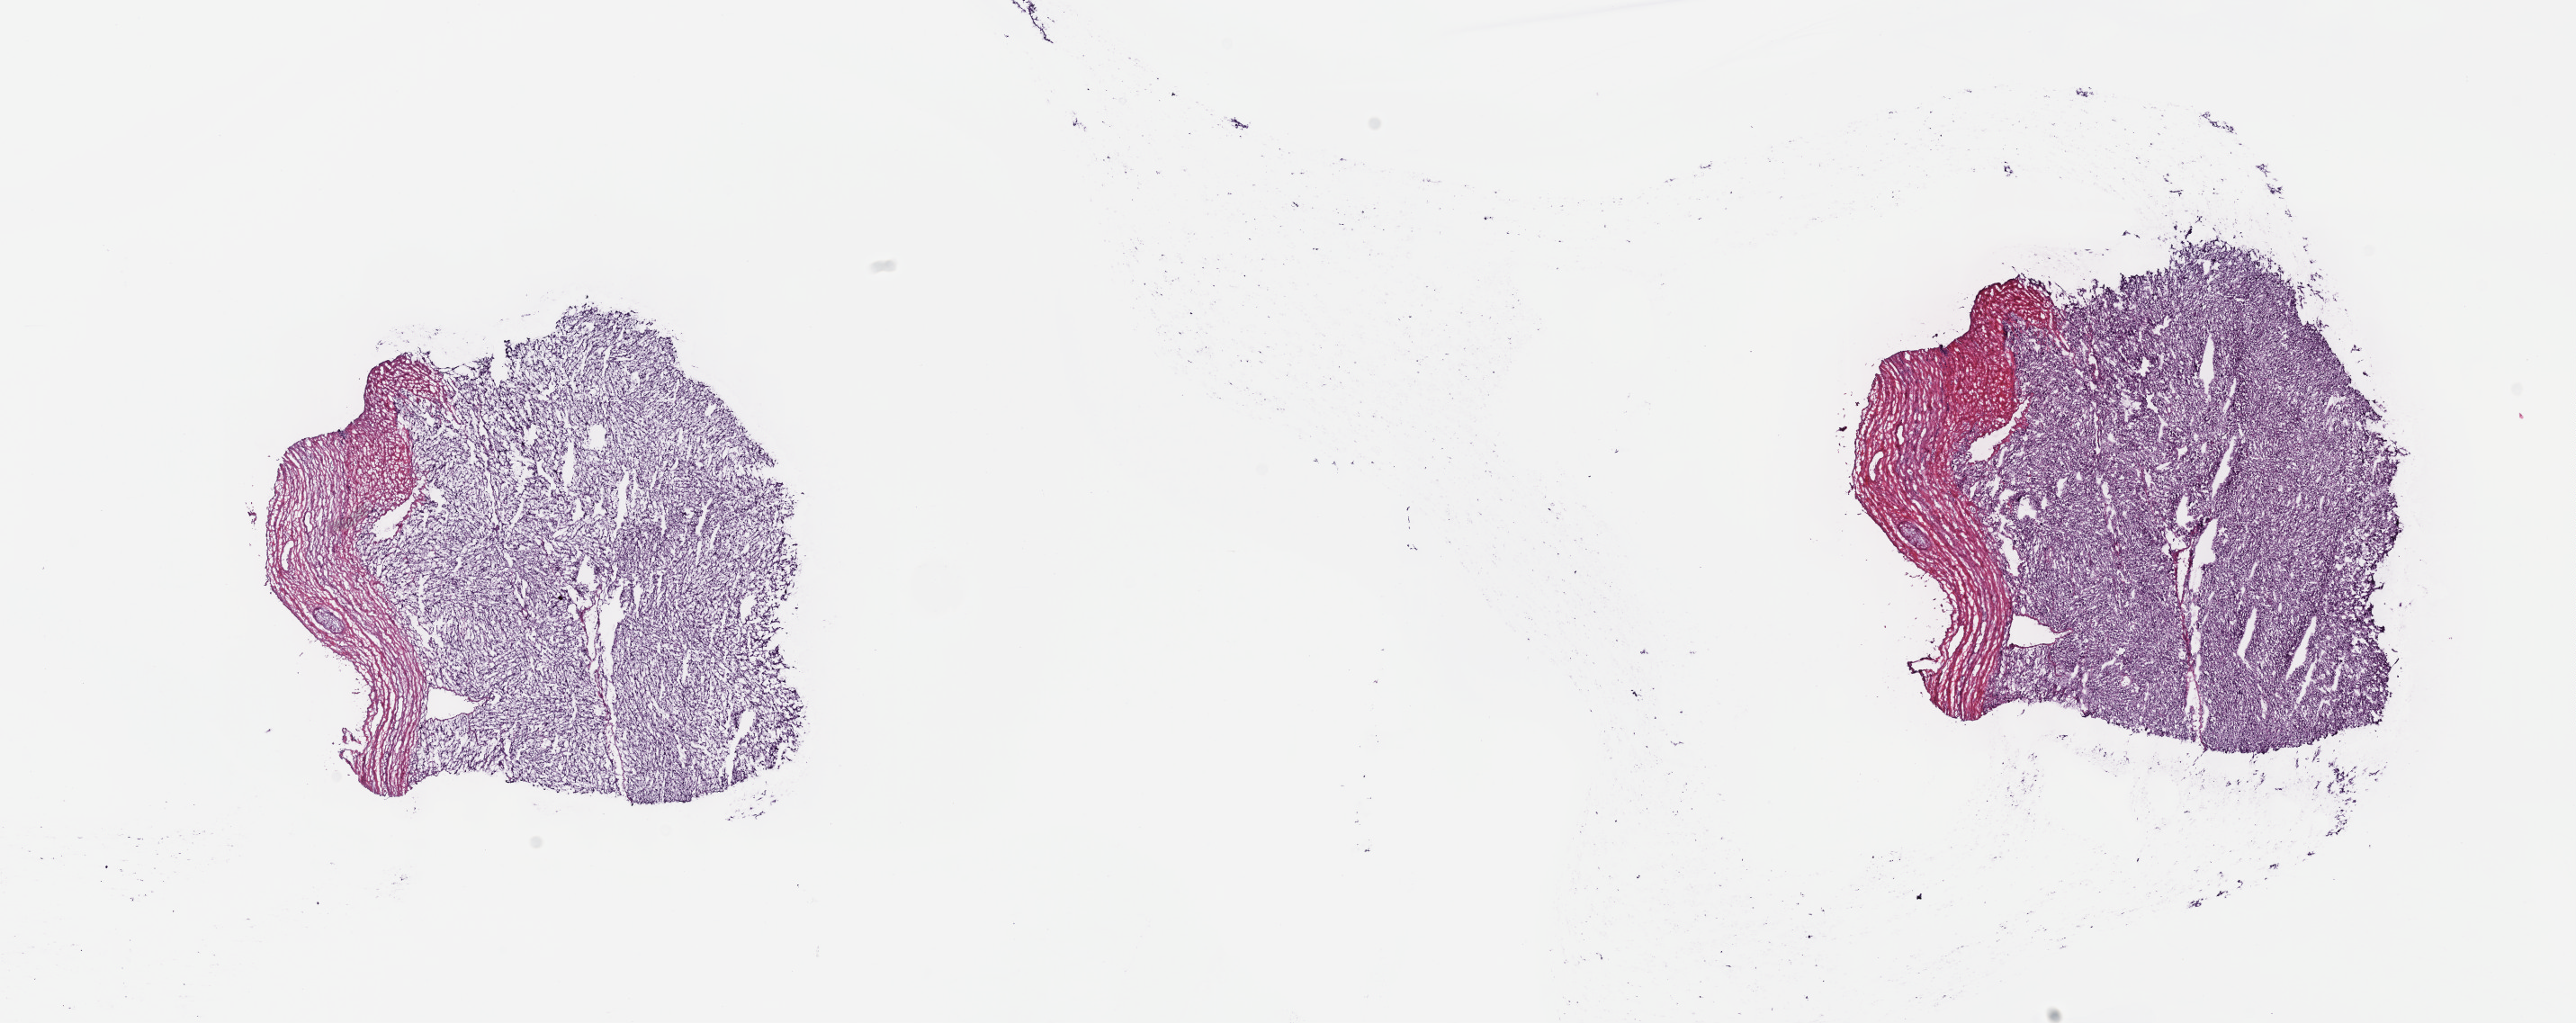
Digitized H&E tissue section (whole slide), shown as a low-resolution overview of the whole scanned area (about 23.2 x 9.2 mm). Frozen section. Adrenal gland, primary tumour sample. Patient: male, age at initial diagnosis 57 years. Composition of this section per pathologist review: tumour cells 80%, tumour nuclei 80%, normal cells 0%, stromal cells 10%, necrosis 10%. Inflammatory infiltration, as recorded: lymphocyte infiltration 40%, monocyte infiltration 20%, neutrophil infiltration 20%.
Diagnosis: Pheochromocytoma, NOS.